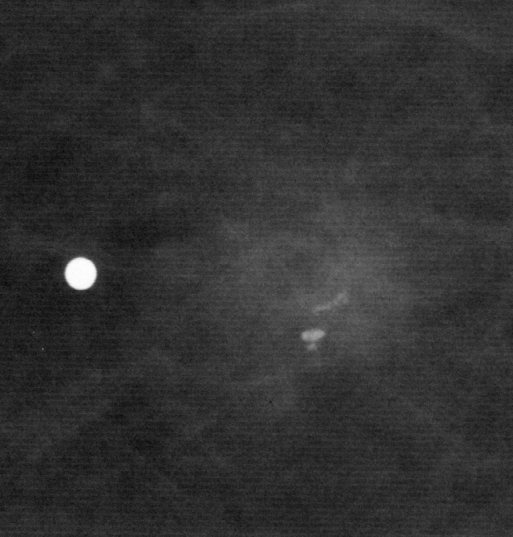
Cropped region of a digitized screen-film mammogram centred on a radiologist-marked abnormality, right breast, CC view, BI-RADS breast density category 1 (scale 1–4).
Finding: calcifications, morphology fine linear branching, distribution clustered; BI-RADS assessment category 4; subtlety rating 5 on a 1 (subtle) to 5 (obvious) scale; pathology (as recorded): benign.